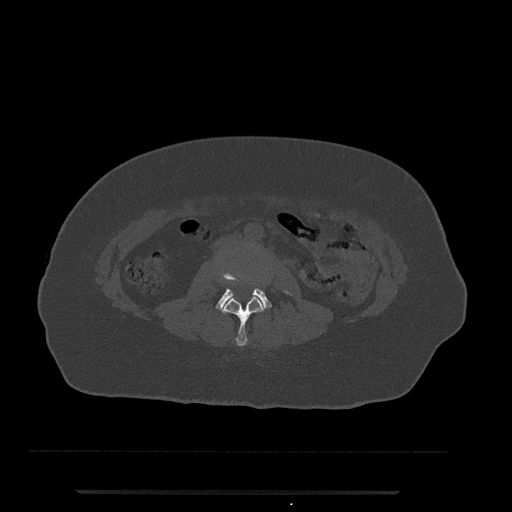
CT including the spine, one axial slice. Position 1 of 797 along the scan axis. Reconstruction kernel Br40s/3. 120 kVp. Bone window (W 1800 / L 400 HU). 0.5 mm slice thickness. 512 × 512 image matrix, field of view 440 × 440 mm. Patient: female, 51 years. From the clinical record (not read from this slice): primary cancer: neuro.
Outlined on this slice (semi-automatic segmentation, software-assisted and operator-edited):
- L2 vertebra: bounding box <222,275,265,346> (left, top, right, bottom; pixels)